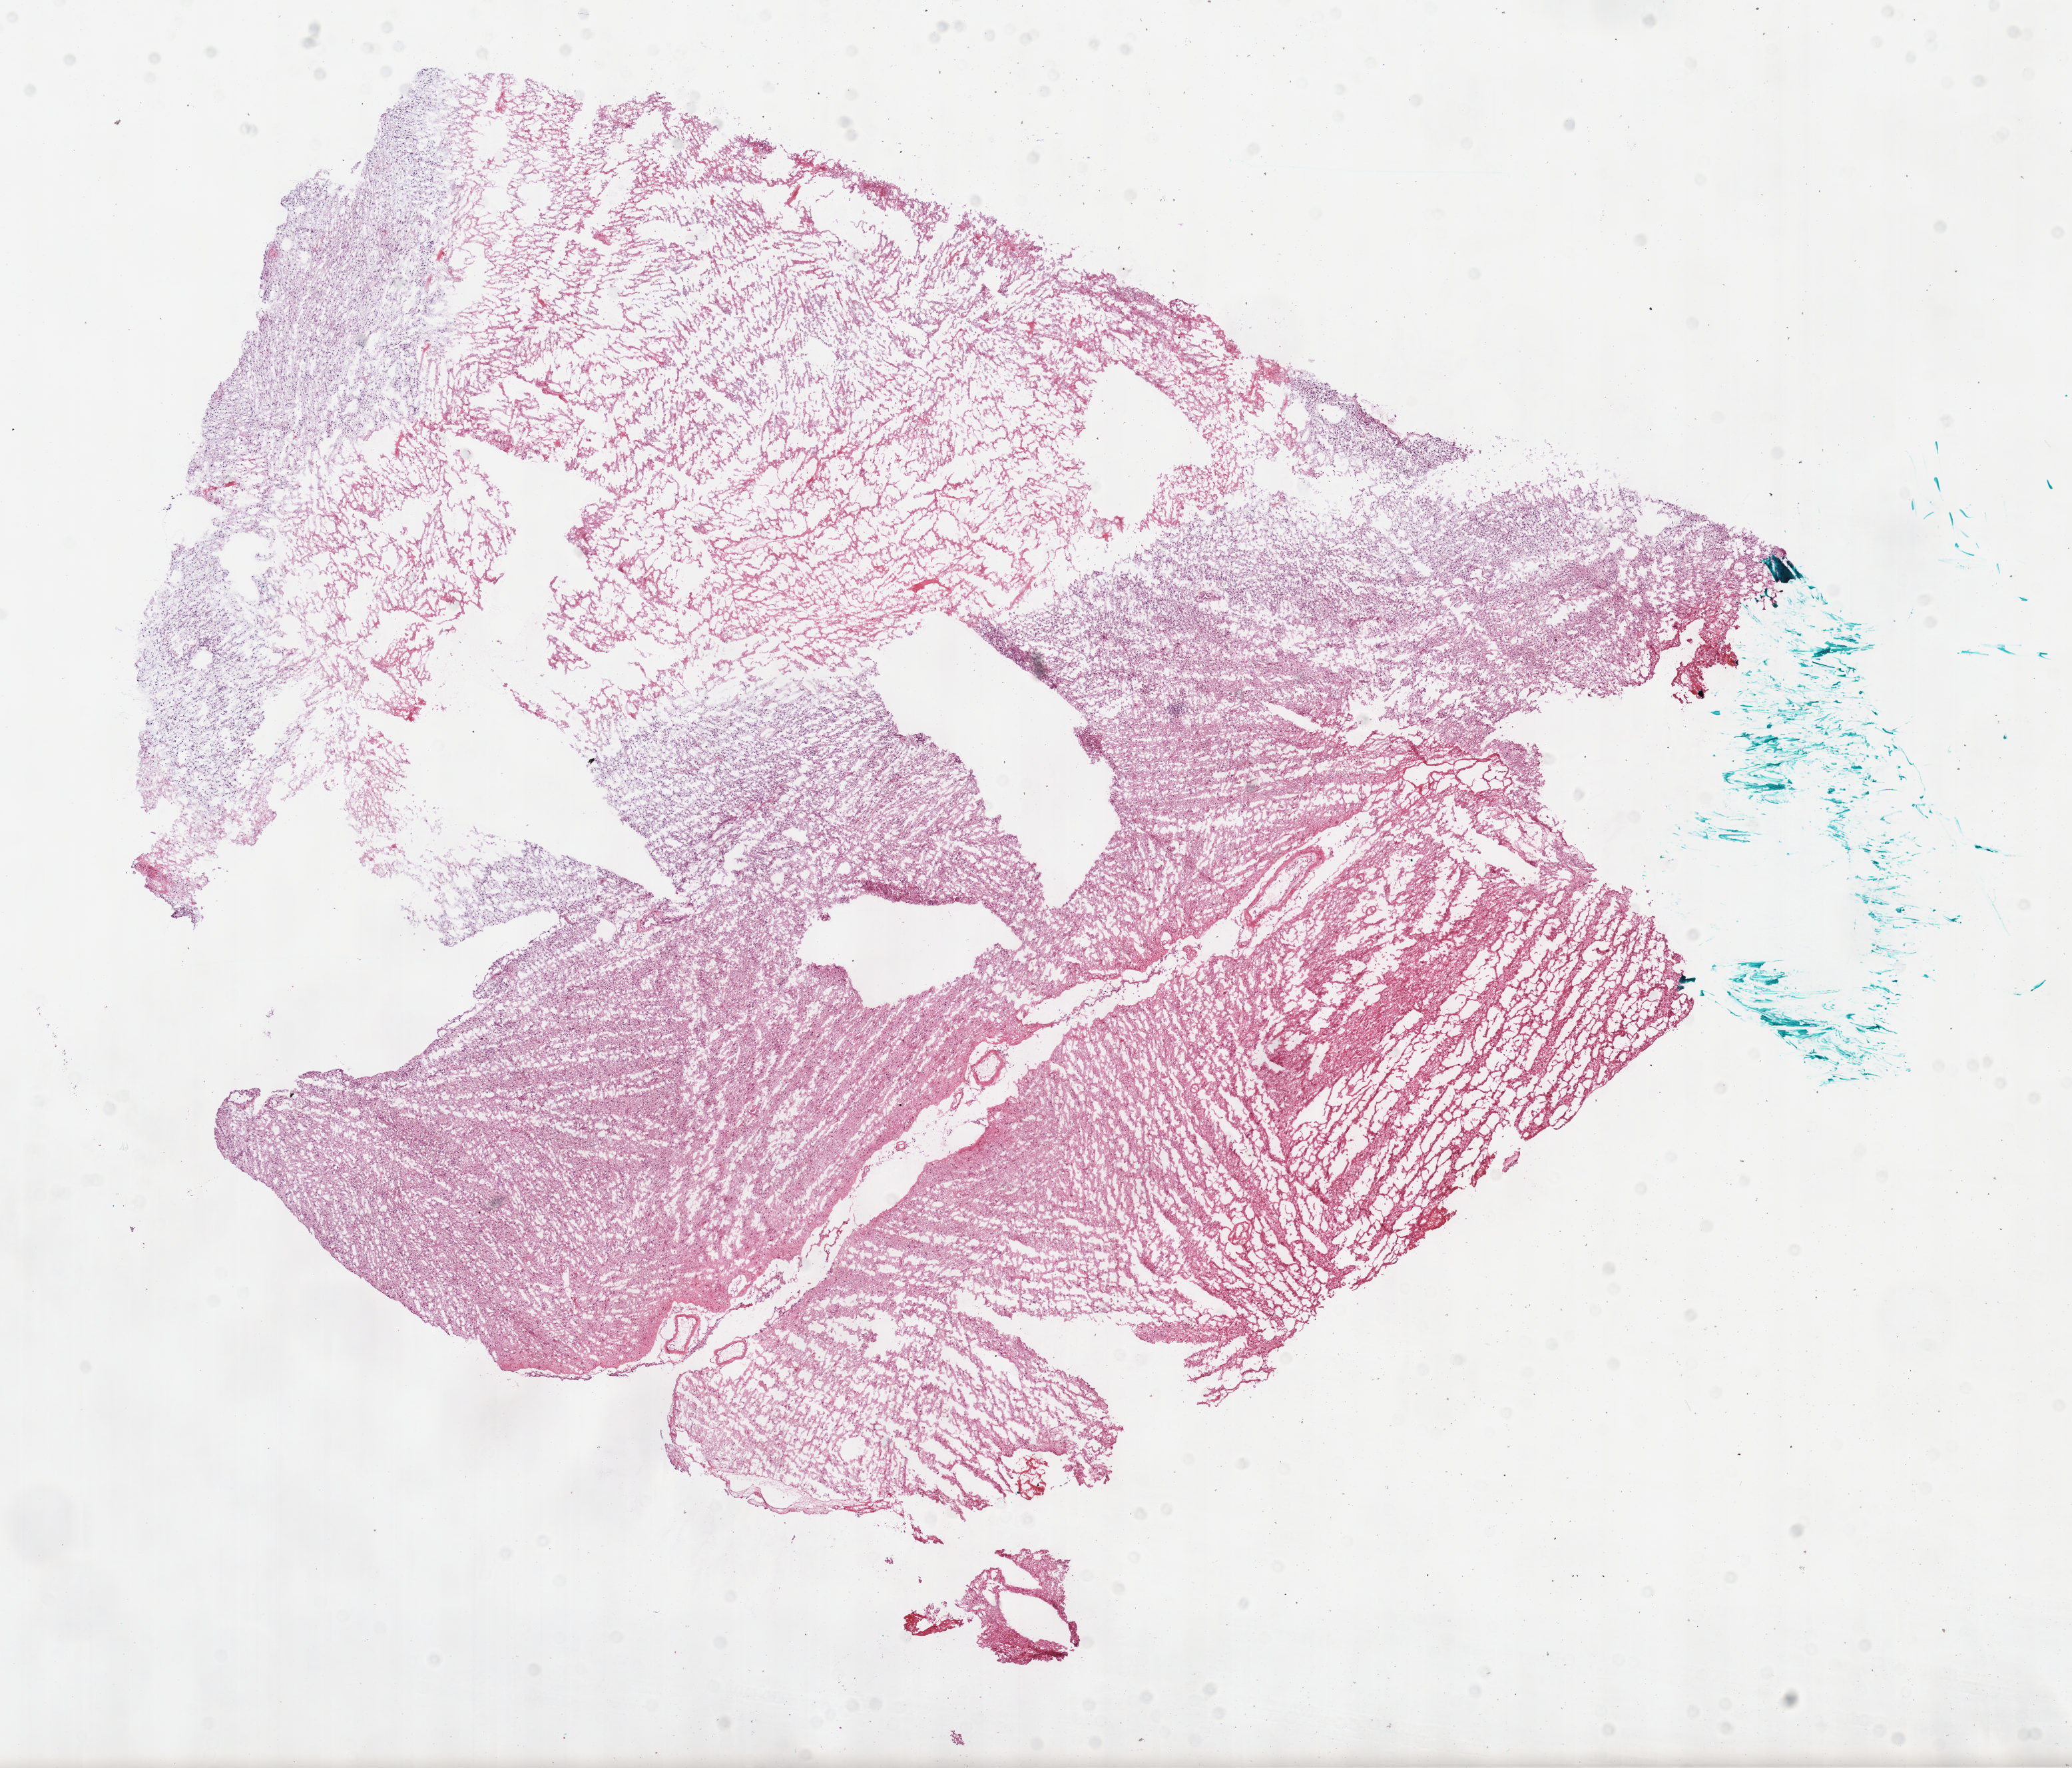
H&E-stained whole-slide image, a low-resolution overview of the entire scanned area, about 12.6 x 10.7 mm. Frozen section from the bottom of the tissue portion. Sample: primary tumour, brain. Male patient; age at initial diagnosis 75 years. Composition of this section per pathologist review: tumour cells 75%, tumour nuclei 100%, normal cells 0%, stromal cells 0%, necrosis 25%. Infiltration values recorded for this section: lymphocyte infiltration 0%.
Diagnosis: Glioblastoma.